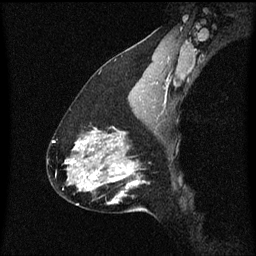
Breast MRI (dynamic contrast-enhanced), one sagittal slice; position 38 of 60 along the scan axis; dynamic contrast-enhanced series, image 2 of 3 at this slice position (ordered by acquisition); 1.5 T; TE 4.2 ms, TR 8.4 ms; 2 mm slice thickness; 256 × 256 image matrix. Patient: female, 47 years.
Annotated regions visible in this slice (semi-automatically segmented with operator editing):
- analysis volume of interest (the breast-tissue region the enhancement analysis was run in; not a lesion): box from (x=81, y=138) to (x=147, y=213) px
- tumour enhancement mask (voxels above the 70 % enhancement threshold inside the analysis volume of interest): (x=81, y=138)–(x=145, y=203)